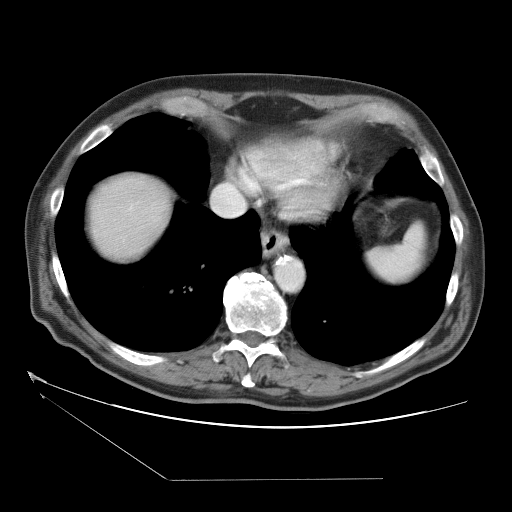
Contrast-enhanced abdominal CT (liver protocol), one axial slice; one of 2 acquisitions stored at this slice position; soft-tissue window (W 400 / L 40 HU); 5 mm slice thickness; 512 × 512 image matrix, field of view 400 × 400 mm. Case-level facts recorded for this patient, not image findings: diagnosis: hepatocellular carcinoma (patient treated with transarterial chemoembolisation; whether this scan precedes or follows treatment is not stated here); TNM stage (as recorded): Stage-II; Child-Pugh class: A; tumour differentiation: moderately differentiated; tumour nodularity: multinodular.
Structures marked on this image (semi-automatically segmented with operator editing):
- liver parenchyma outside the tumour (the mass and vessels are separate outlines, so this box may not span the whole liver): bounding box [x1, y1, x2, y2] px = [92, 174, 170, 256]